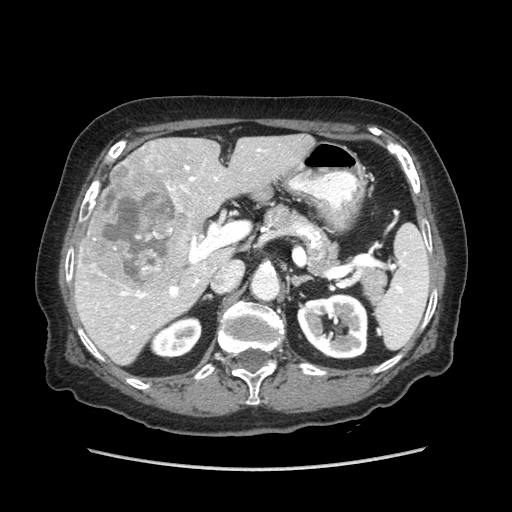
Contrast-enhanced abdominal CT (liver protocol), one axial slice. Position 44 of 89 along the scan axis. Soft-tissue window (W 400 / L 40 HU). 2.5 mm slice thickness. 512 × 512 image matrix, field of view 360 × 360 mm. Case-level facts recorded for this patient, not image findings: diagnosis: hepatocellular carcinoma (patient treated with transarterial chemoembolisation; whether this scan precedes or follows treatment is not stated here); TNM stage (as recorded): Stage-IIIA; Child-Pugh class: A; tumour differentiation: well differentiated; tumour nodularity: multinodular.
Annotated regions visible in this slice (semi-automatically segmented with operator editing):
- liver parenchyma outside the tumour (the mass and vessels are separate outlines, so this box may not span the whole liver): bounding box [x1, y1, x2, y2] px = [74, 134, 314, 364]
- mass: [80, 164, 195, 295]
- liver vessels: [107, 149, 261, 330]